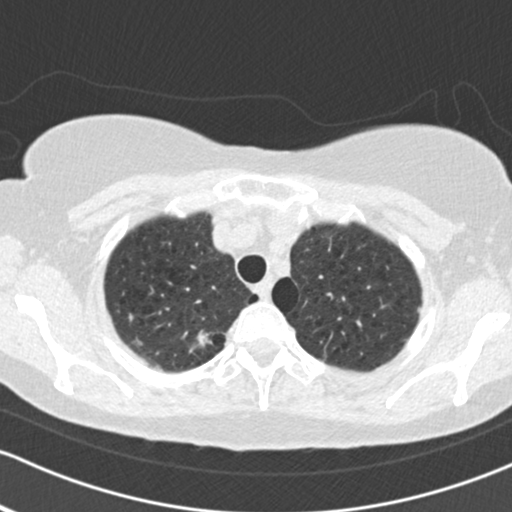
Low-dose screening chest CT, one axial slice. Position 140 of 161 along the scan axis. Reconstruction kernel B30f. 120 kVp. Lung window (W 1500 / L -600 HU). 2 mm slice thickness. 512 × 512 image matrix, field of view 312 × 312 mm.
Structures marked on this image (expert manual segmentation):
- lesion 1 (tumor, upper lobe of right lung): bounding box [x1, y1, x2, y2] px = [189, 330, 212, 353]